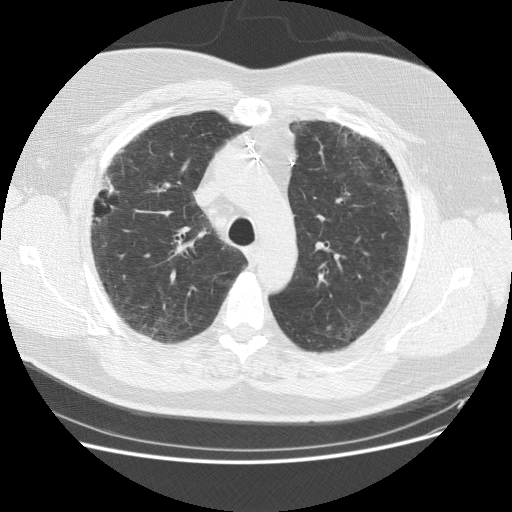
Chest CT (low-dose screening protocol), one axial image. Baseline screening round. Lung window (W 1500 / L -600 HU). 2.5 mm slice thickness. Male participant, aged 59 years at enrolment. Current smoker at enrolment.
• Expert reader's lesion annotation, bounding box [x1, y1, x2, y2] px = [77, 160, 138, 242].
• The screening reader recorded 2 non-calcified nodules or masses ≥4 mm on this exam (right middle lobe, right lower lobe); which of them this box marks is not recorded.
• Lung cancer was diagnosed 338 days after this screen: adenocarcinoma, NOS, right upper lobe, right middle lobe, moderately differentiated (G2), stage IA (AJCC 6th edition), 13 mm at pathology.